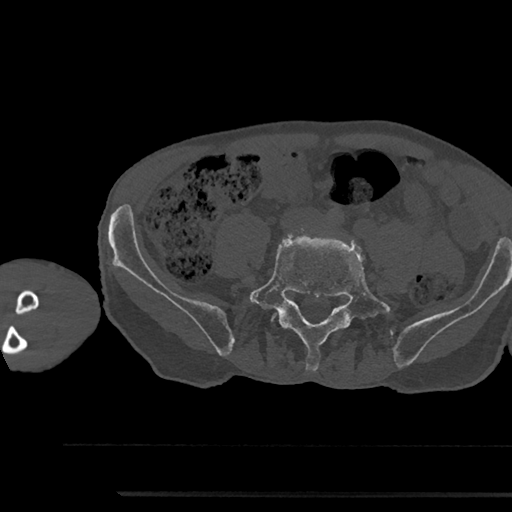
CT including the spine, one axial slice; slice 351 of 797 in the series (ordered by position); 120 kVp; bone window (W 1800 / L 400 HU); 0.5 mm slice thickness; 512 × 512 image matrix, field of view 367 × 367 mm. Male patient, age 79 years. Case-level facts recorded for this patient, not image findings: primary cancer: prostate.
Annotated regions visible in this slice (semi-automatically segmented with operator editing):
- L5 vertebra: bounding box <243,236,393,371> (left, top, right, bottom; pixels)